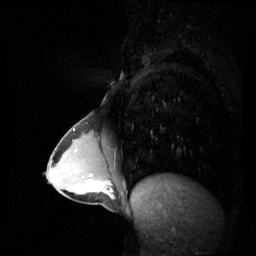
Breast MRI (dynamic contrast-enhanced), one sagittal slice; position 26 of 60 along the scan axis; dynamic contrast-enhanced series, image 2 of 3 at this slice position (ordered by acquisition); 1.5 T; TE 4.2 ms, TR 8.9 ms; 2.4 mm slice thickness; 256 × 256 image matrix, field of view 300 × 300 mm. Female patient, age 34 years. From the clinical record (not read from this slice): setting: breast cancer imaged before/during neoadjuvant chemotherapy; receptor status: triple-negative.
Outlined on this slice (semi-automatically segmented with operator editing):
- analysis volume of interest (the breast-tissue region the enhancement analysis was run in; not a lesion): bounding box [x1, y1, x2, y2] px = [65, 168, 113, 204]
- tumour enhancement mask (voxels above the 70 % enhancement threshold inside the analysis volume of interest): [91, 187, 98, 191]